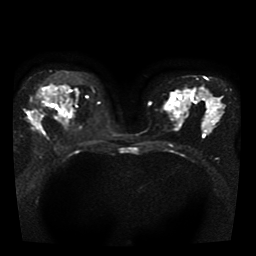
Breast MRI, one axial slice; slice 25 of 41 in the series (ordered by position); diffusion-weighted series; image 2 of 4 stored at this slice position (different b-values; order by instance number); 1.5 T; 256 × 256 image matrix. Female patient.
Annotated regions visible in this slice (expert manual segmentation):
- tumour on diffusion-weighted imaging: box from (x=29, y=96) to (x=42, y=131) px